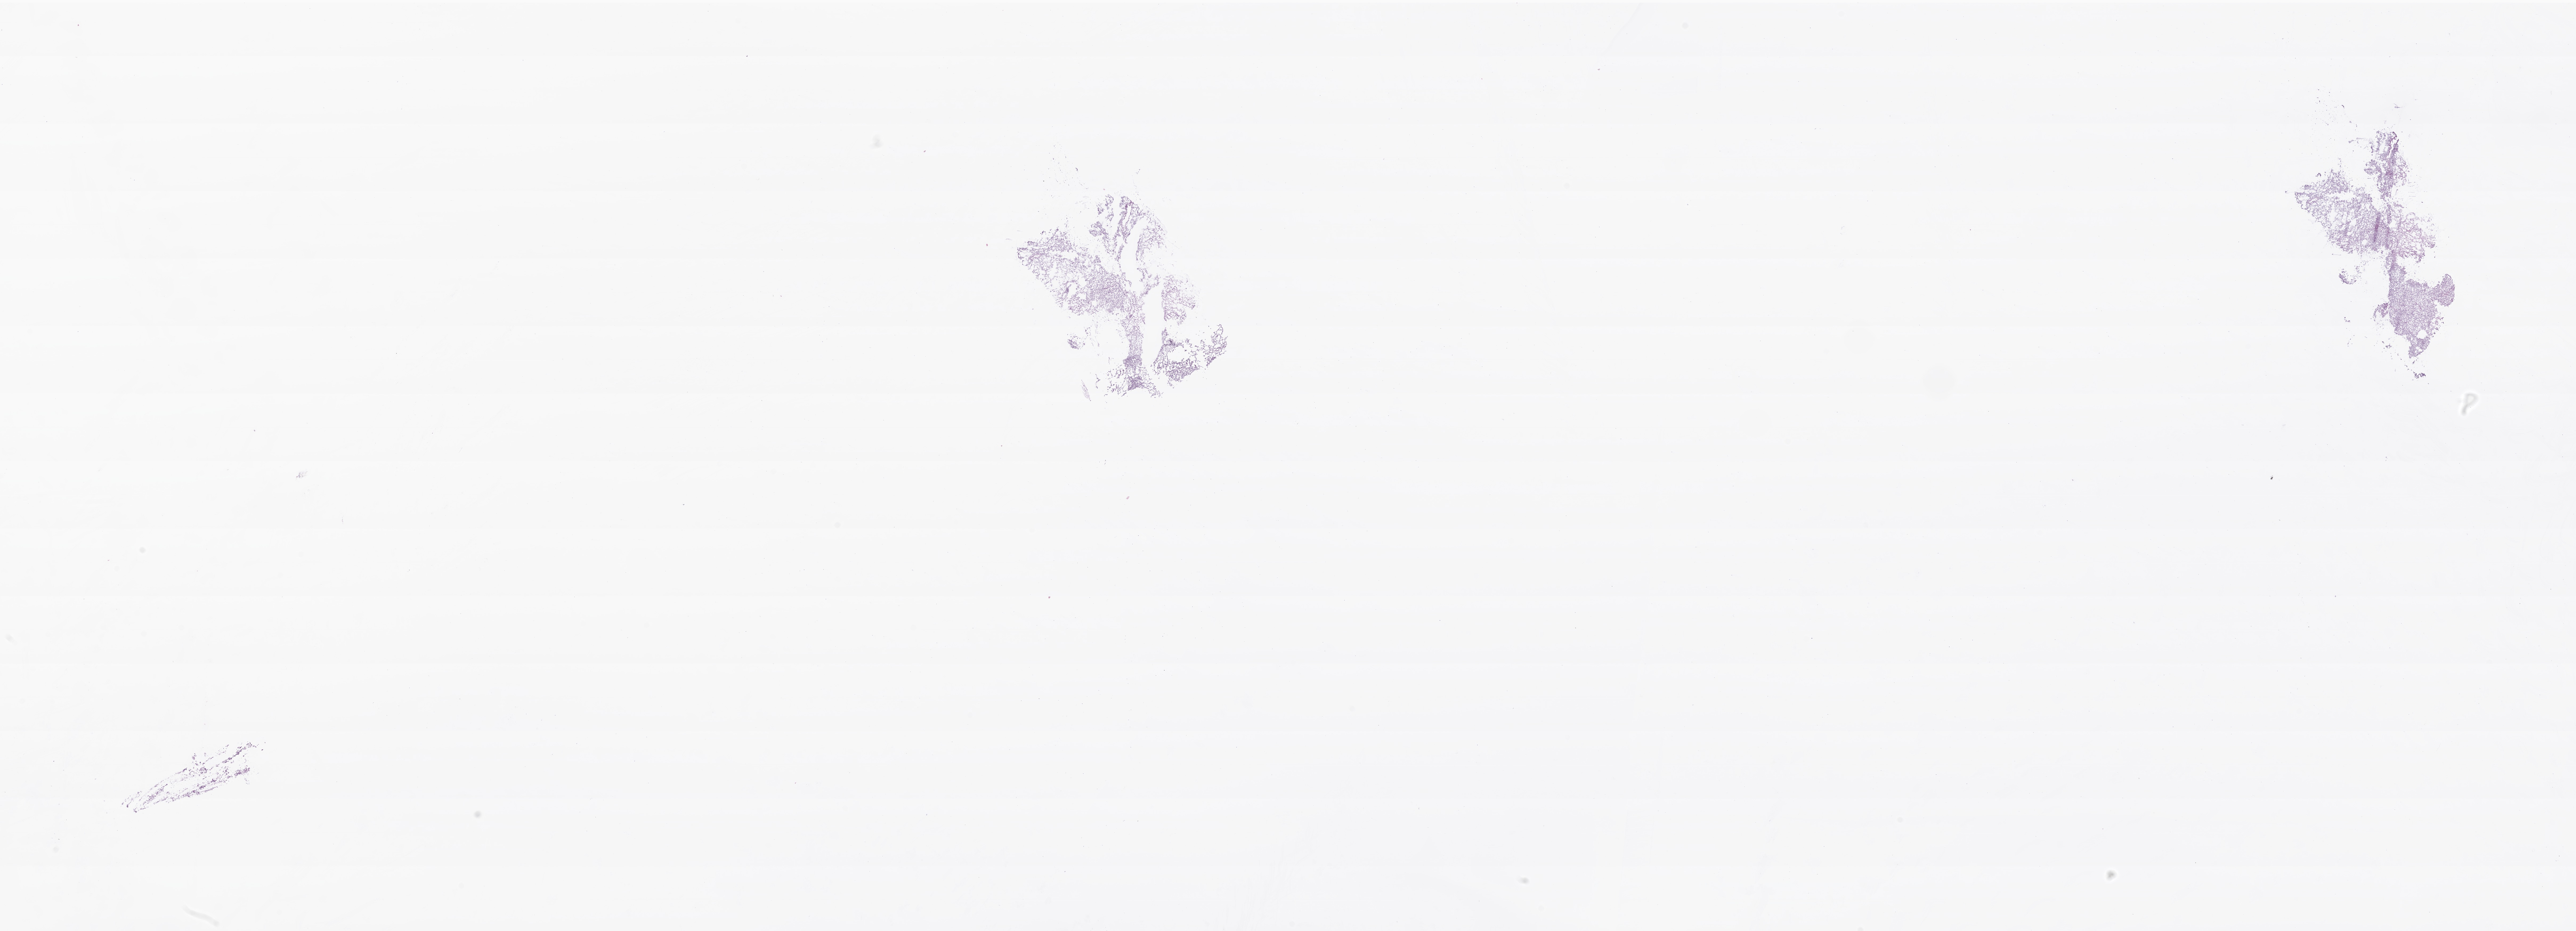
Hematoxylin and eosin (H&E) whole-slide image of tumor tissue from the parotid gland — whole scanned area (about 40.6 x 14.7 mm) shown as a low-resolution overview; frozen section. Patient: male, age 172 months (14 years 4 months).
Diagnosis: Epithelial-myoepithelial carcinoma.